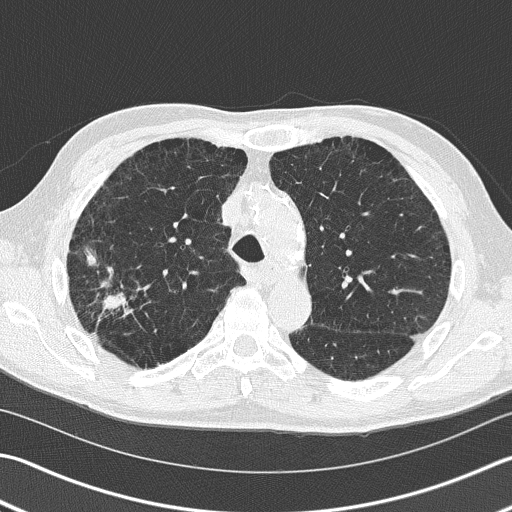
Low-dose screening chest CT, one axial slice; slice 111 of 163 in the series (ordered by position); lung window (W 1500 / L -600 HU); 512 × 512 image matrix, field of view 346 × 346 mm.
Annotated regions visible in this slice (outlined manually by an expert reader):
- lesion 1 (tumor, upper lobe of right lung): bounding box [x1, y1, x2, y2] px = [88, 254, 129, 314]